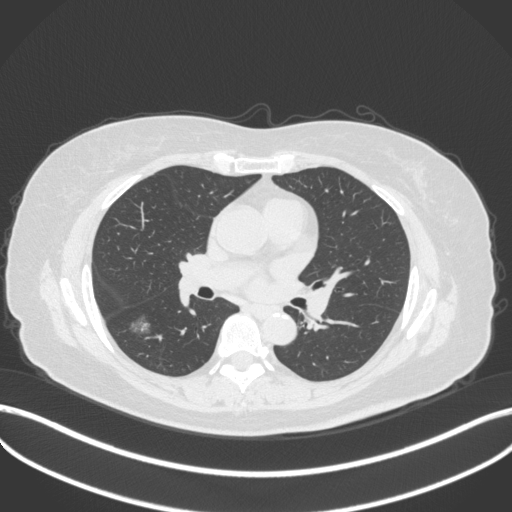
Chest CT, one axial slice; slice 171 of 322 in the series (ordered by position); lung window (W 1500 / L -600 HU); 1 mm slice thickness; 512 × 512 image matrix, field of view 400 × 400 mm. Female patient, age 64 years. Case-level facts recorded for this patient, not image findings: clinical TNM (as recorded): T1c N0 M0; histopathological grade: G1.
Outlined on this slice (bounding box drawn by a radiologist):
- lung tumour (recorded histology: adenocarcinoma): box from (x=125, y=311) to (x=154, y=337) px